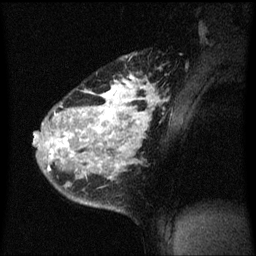
Breast MRI (dynamic contrast-enhanced), one sagittal slice. Slice 46 of 60 in the series (ordered by position). Dynamic contrast-enhanced series, image 2 of 3 at this slice position (ordered by acquisition). 1.5 T. TE 4.2 ms, TR 8.4 ms. 2 mm slice thickness. 256 × 256 image matrix, field of view 200 × 200 mm. Patient: female, 34 years. Case-level facts recorded for this patient, not image findings: setting: breast cancer imaged before/during neoadjuvant chemotherapy; receptor status: HR-positive, HER2-negative.
Structures marked on this image (semi-automatically segmented with operator editing):
- analysis volume of interest (the breast-tissue region the enhancement analysis was run in; not a lesion): box from (x=34, y=52) to (x=163, y=213) px
- tumour enhancement mask (voxels above the 70 % enhancement threshold inside the analysis volume of interest): (x=36, y=76)–(x=157, y=173)